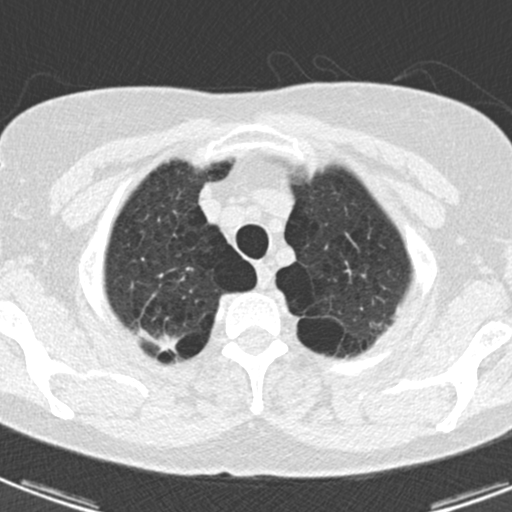
Low-dose screening chest CT, one axial slice; slice 155 of 174 in the series (ordered by position); 120 kVp; lung window (W 1500 / L -600 HU); 512 × 512 image matrix.
Structures marked on this image (outlined manually by an expert reader):
- lesion 1 (tumor, upper lobe of right lung): box from (x=155, y=334) to (x=178, y=353) px